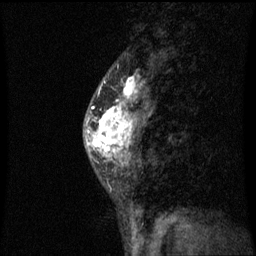
Breast MRI (dynamic contrast-enhanced), one sagittal slice. Position 27 of 60 along the scan axis. Dynamic contrast-enhanced series, image 2 of 3 at this slice position (ordered by acquisition). 1.5 T. TE 4.2 ms, TR 8.9 ms. 2 mm slice thickness. 256 × 256 image matrix, field of view 200 × 200 mm. Female patient, age 50 years. From the clinical record (not read from this slice): setting: breast cancer imaged before/during neoadjuvant chemotherapy; receptor status: triple-negative.
Structures marked on this image (semi-automatically segmented with operator editing):
- analysis volume of interest (the breast-tissue region the enhancement analysis was run in; not a lesion): box from (x=84, y=80) to (x=149, y=171) px
- tumour enhancement mask (voxels above the 70 % enhancement threshold inside the analysis volume of interest): (x=86, y=80)–(x=139, y=165)